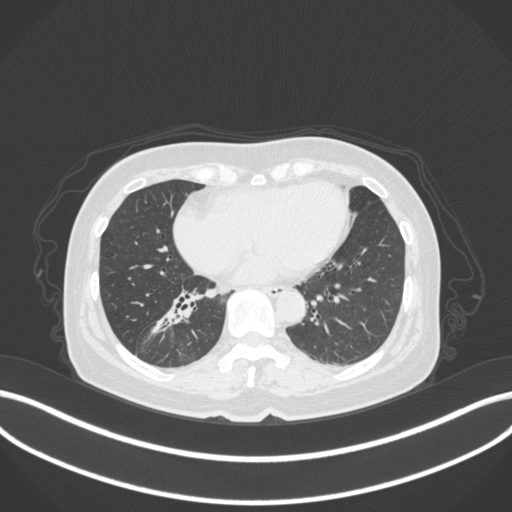
Chest CT, one axial slice; slice 151 of 429 in the series (ordered by position); reconstruction kernel B31f; 120 kVp; lung window (W 1500 / L -600 HU); 512 × 512 image matrix, field of view 400 × 400 mm. Female patient, age 67 years. Case-level facts recorded for this patient, not image findings: clinical TNM (as recorded): T1c N1 M0; histopathological grade: G2-3.
Structures marked on this image (bounding box drawn by a radiologist):
- lung tumour (recorded histology: adenocarcinoma): box from (x=144, y=296) to (x=199, y=336) px